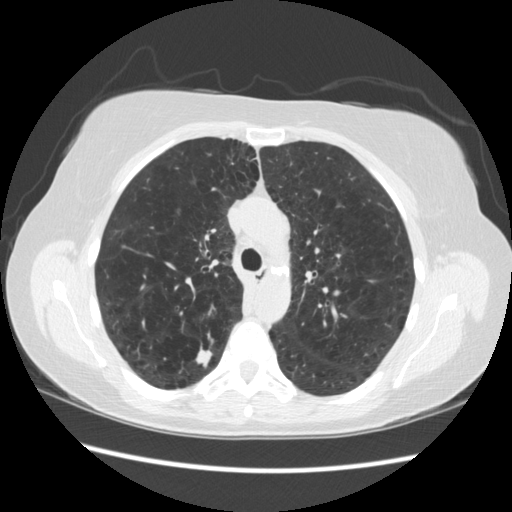
Low-dose screening chest CT, axial slice; third annual screen; lung window (W 1500 / L -600 HU); 2.5 mm slice thickness; standard (soft-tissue) reconstruction kernel (STANDARD). Female participant, aged 55 years at enrolment. Current smoker at enrolment.
• Expert reader's lesion annotation, box from (x=182, y=333) to (x=228, y=374) px.
• The exam's reader record, not a measurement of the box and not confirmed to be the same lesion: non-calcified nodule or mass ≥4 mm, right upper lobe, 11 × 11 mm, poorly defined margins, soft tissue attenuation, pre-existing on the prior screen: no.
• Later outcome: lung cancer diagnosed 96 days after this screen — small cell carcinoma, NOS, right upper lobe.